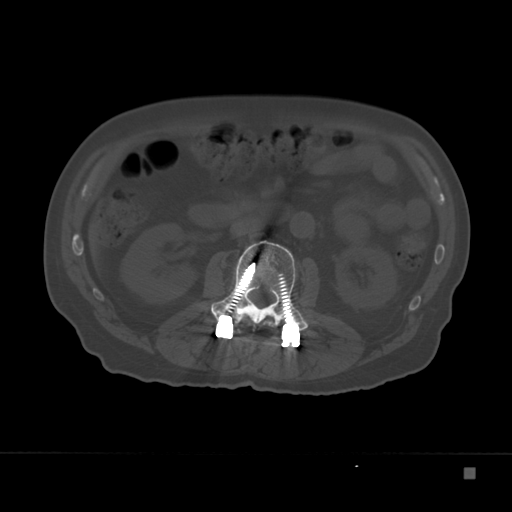
CT including the spine, one axial slice; slice 91 of 332 in the series (ordered by position); 120 kVp; bone window (W 1800 / L 400 HU); 1.5 mm slice thickness; 512 × 512 image matrix, field of view 389 × 389 mm. Male patient, age 72 years. From the clinical record (not read from this slice): primary cancer: skeletal.
Annotated regions visible in this slice (semi-automatic segmentation, software-assisted and operator-edited):
- L1 vertebra: bounding box (x1, y1, x2, y2) in pixels: (241, 320, 275, 328)
- L2 vertebra: (211, 241, 316, 331)